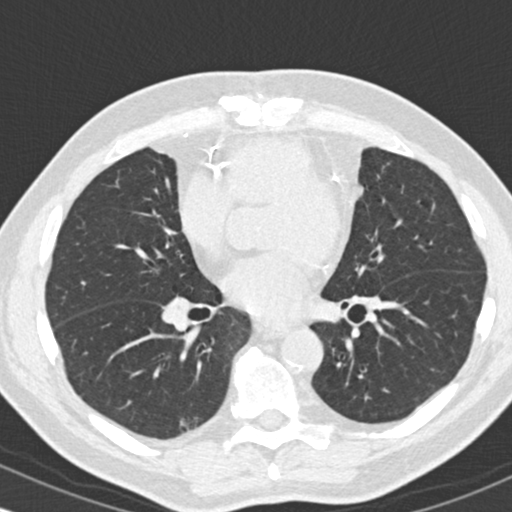
Low-dose screening chest CT, axial slice; second screening round (one year after baseline); lung window (W 1500 / L -600 HU); standard (soft-tissue) reconstruction kernel (B30f); 120 kVp; slice 98 of 180 in the series; 512 × 512 image matrix, field of view 318 × 318 mm. Male, age 68 years at enrolment.
Expert-annotated lung lesion, box from (x=163, y=405) to (x=222, y=446) px. The screening reader recorded 2 non-calcified nodules or masses ≥4 mm on this exam (lingula, right upper lobe); which of them this box marks is not recorded. Lung cancer was diagnosed 476 days after this screen: adenosquamous carcinoma, right lower lobe, moderately differentiated (G2), stage IB (AJCC 6th edition), 31 mm at pathology.